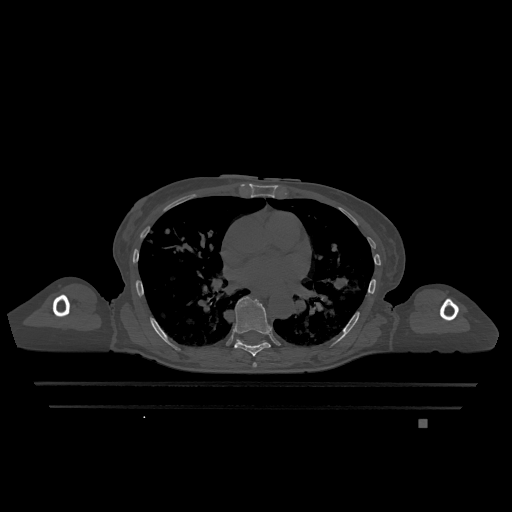
CT including the spine, one axial slice; slice 732 of 1317 in the series (ordered by position); bone window (W 1800 / L 400 HU); 0.5 mm slice thickness; 512 × 512 image matrix, field of view 500 × 500 mm. Female patient, age 74 years. Case-level facts recorded for this patient, not image findings: primary cancer: lung; vertebrae with lytic lesions (as recorded): T1, T4, T5, T6, L4, L5.
Structures marked on this image (semi-automatically segmented with operator editing):
- T6 vertebra: bounding box <253,362,257,368> (left, top, right, bottom; pixels)
- T7 vertebra: <234,296,271,356>
- T9 vertebra: <236,340,267,343>